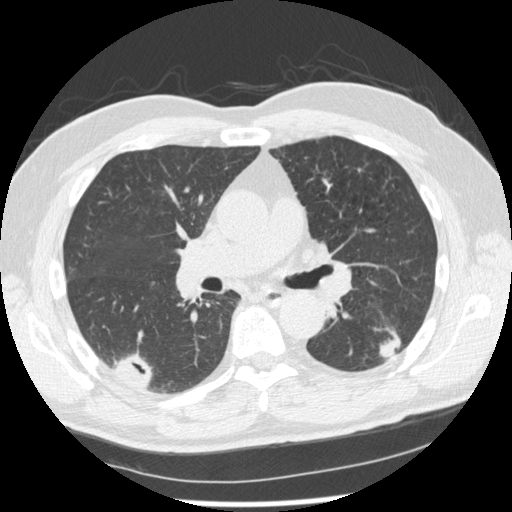
Low-dose screening chest CT, axial slice, second screening round (one year after baseline), lung window (W 1500 / L -600 HU), 1.25 mm slice thickness, standard (soft-tissue) reconstruction kernel (STANDARD), 120 kVp, 512 × 512 image matrix. Male, age 74 years at enrolment. Former smoker at enrolment.
- Lesion marked by an expert reader, box from (x=372, y=316) to (x=421, y=368) px.
- The screening reader recorded 7 non-calcified nodules or masses ≥4 mm on this exam (right upper lobe, right lower lobe, right upper lobe, right lower lobe, left lower lobe, left upper lobe, left upper lobe); which of them this box marks is not recorded.